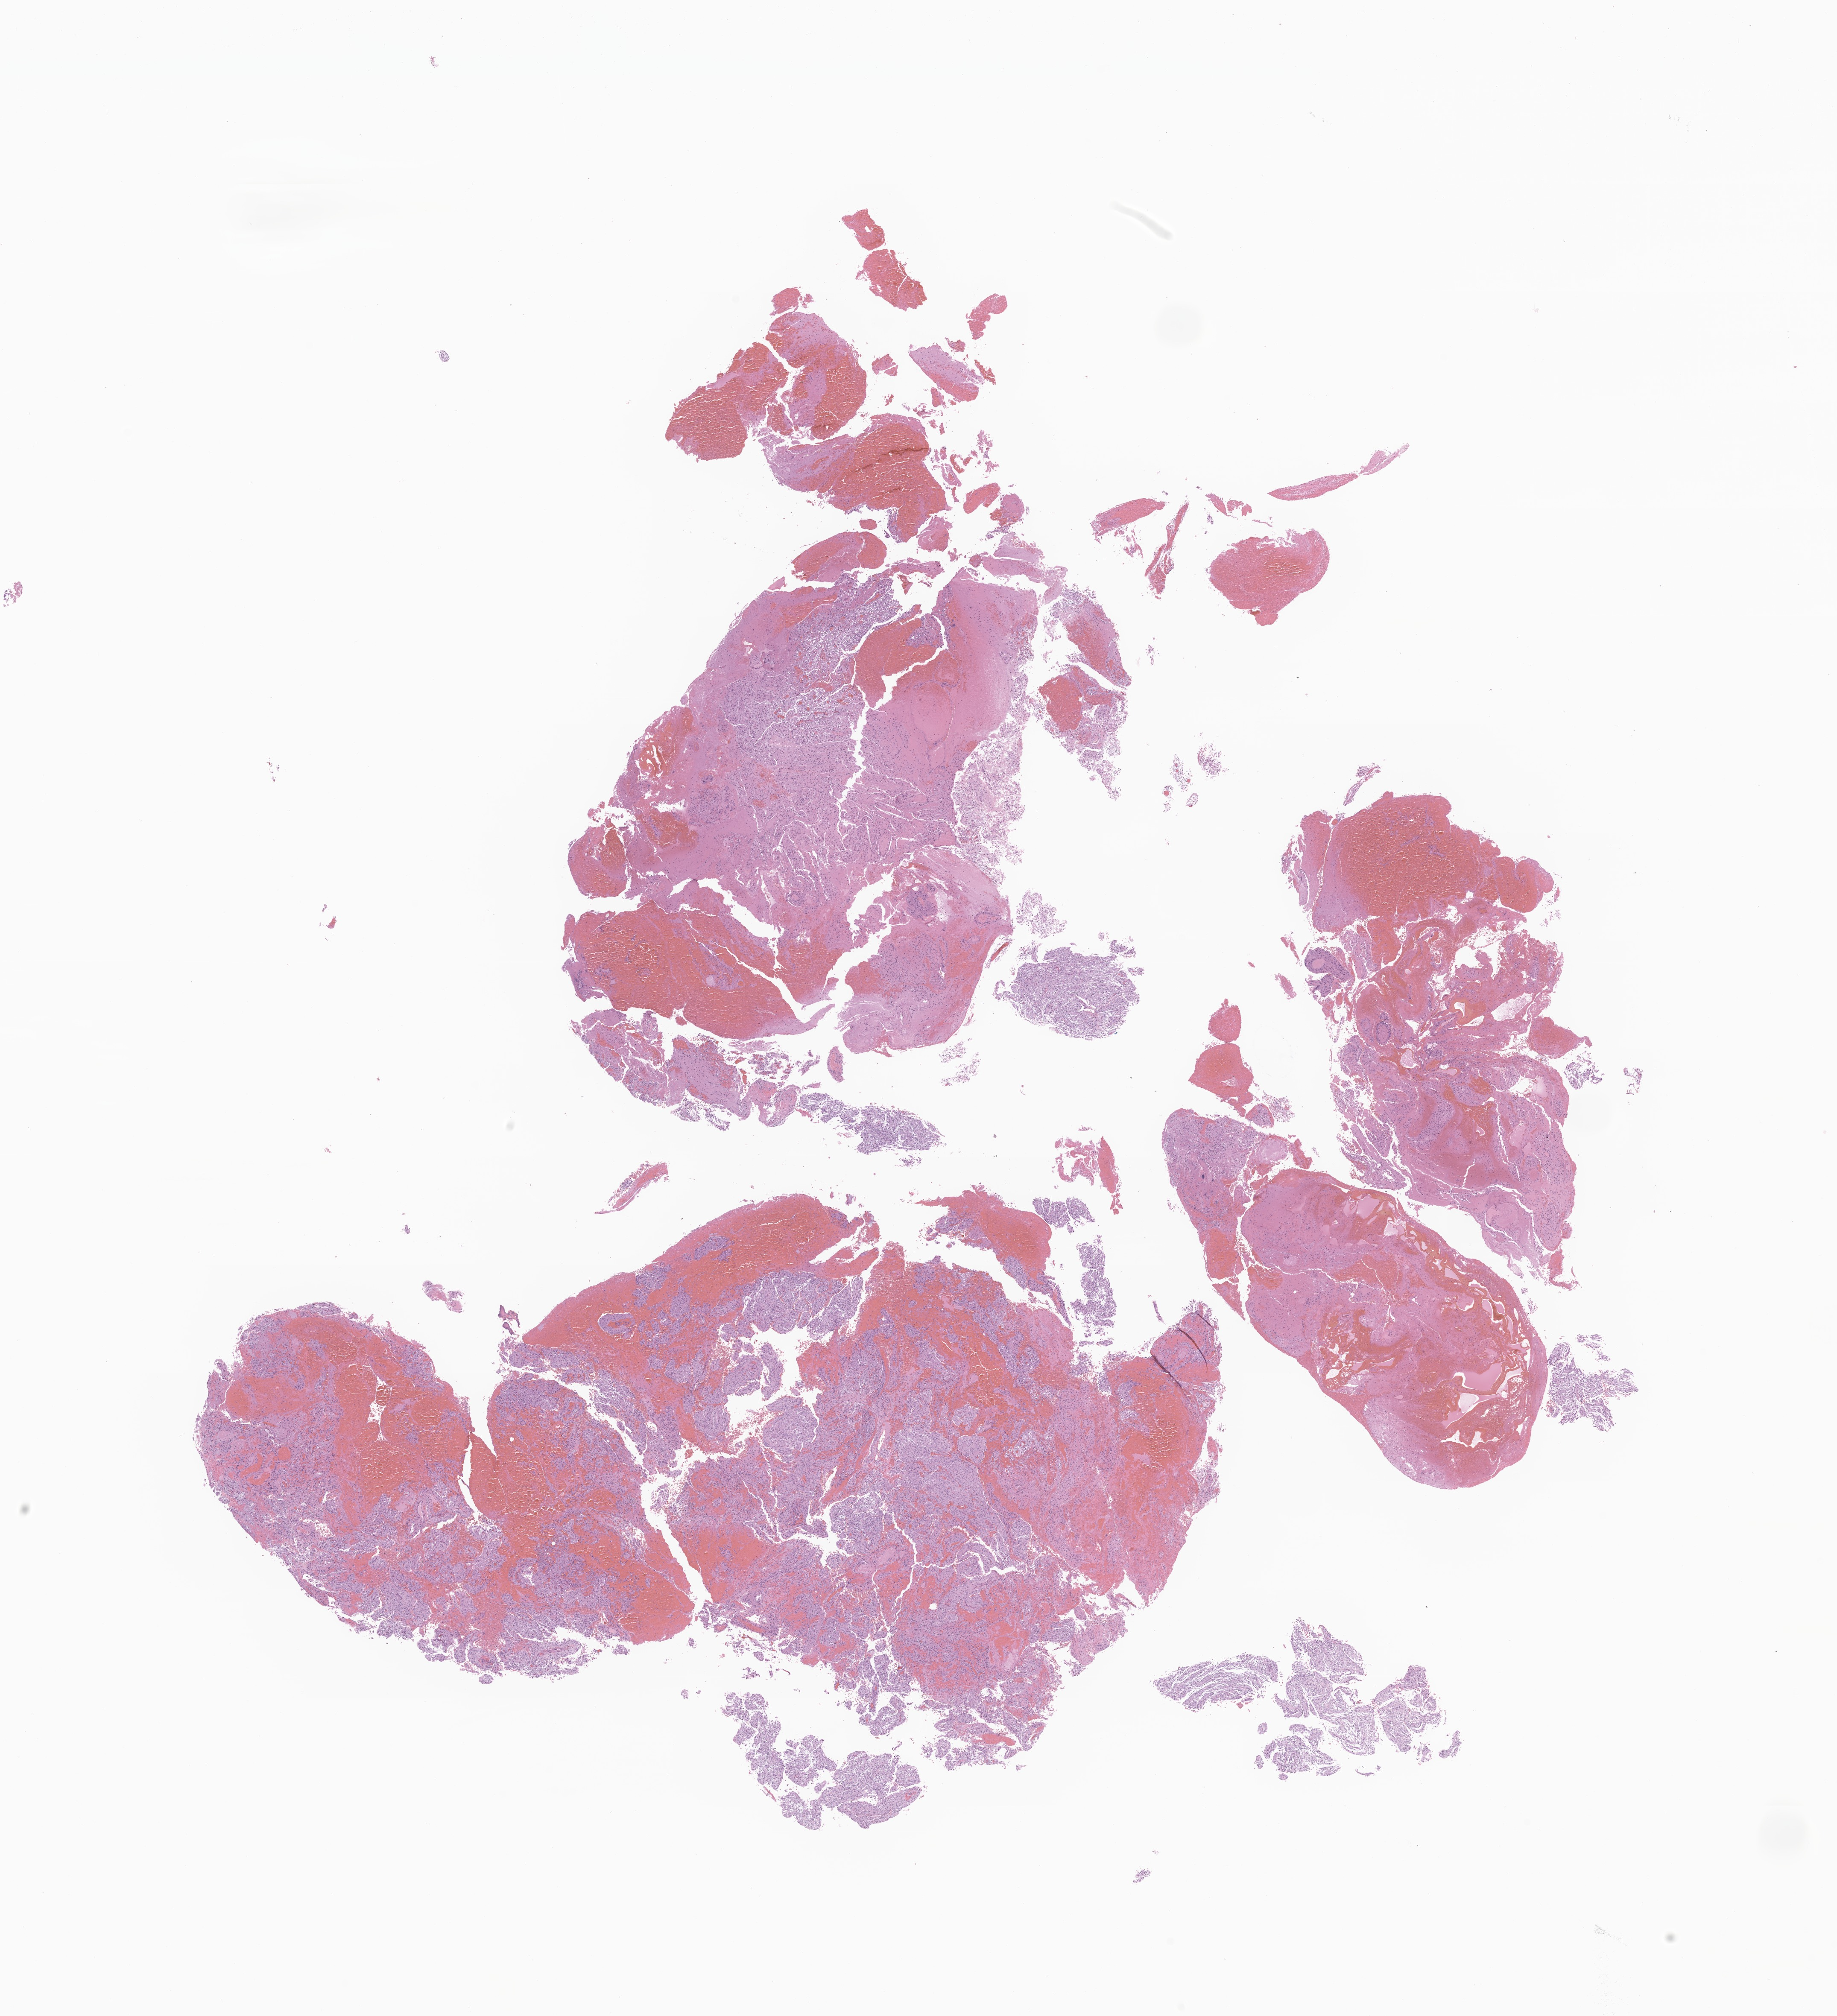
Haematoxylin and eosin whole-slide image of tumor tissue from the brain, a low-resolution overview of the entire scanned area, about 18.1 x 19.9 mm. Formalin-fixed, paraffin-embedded (FFPE) tissue. Female patient, age 60 months (5 years).
• diagnosis (ICD-O-3 morphology term): Pilocytic astrocytoma